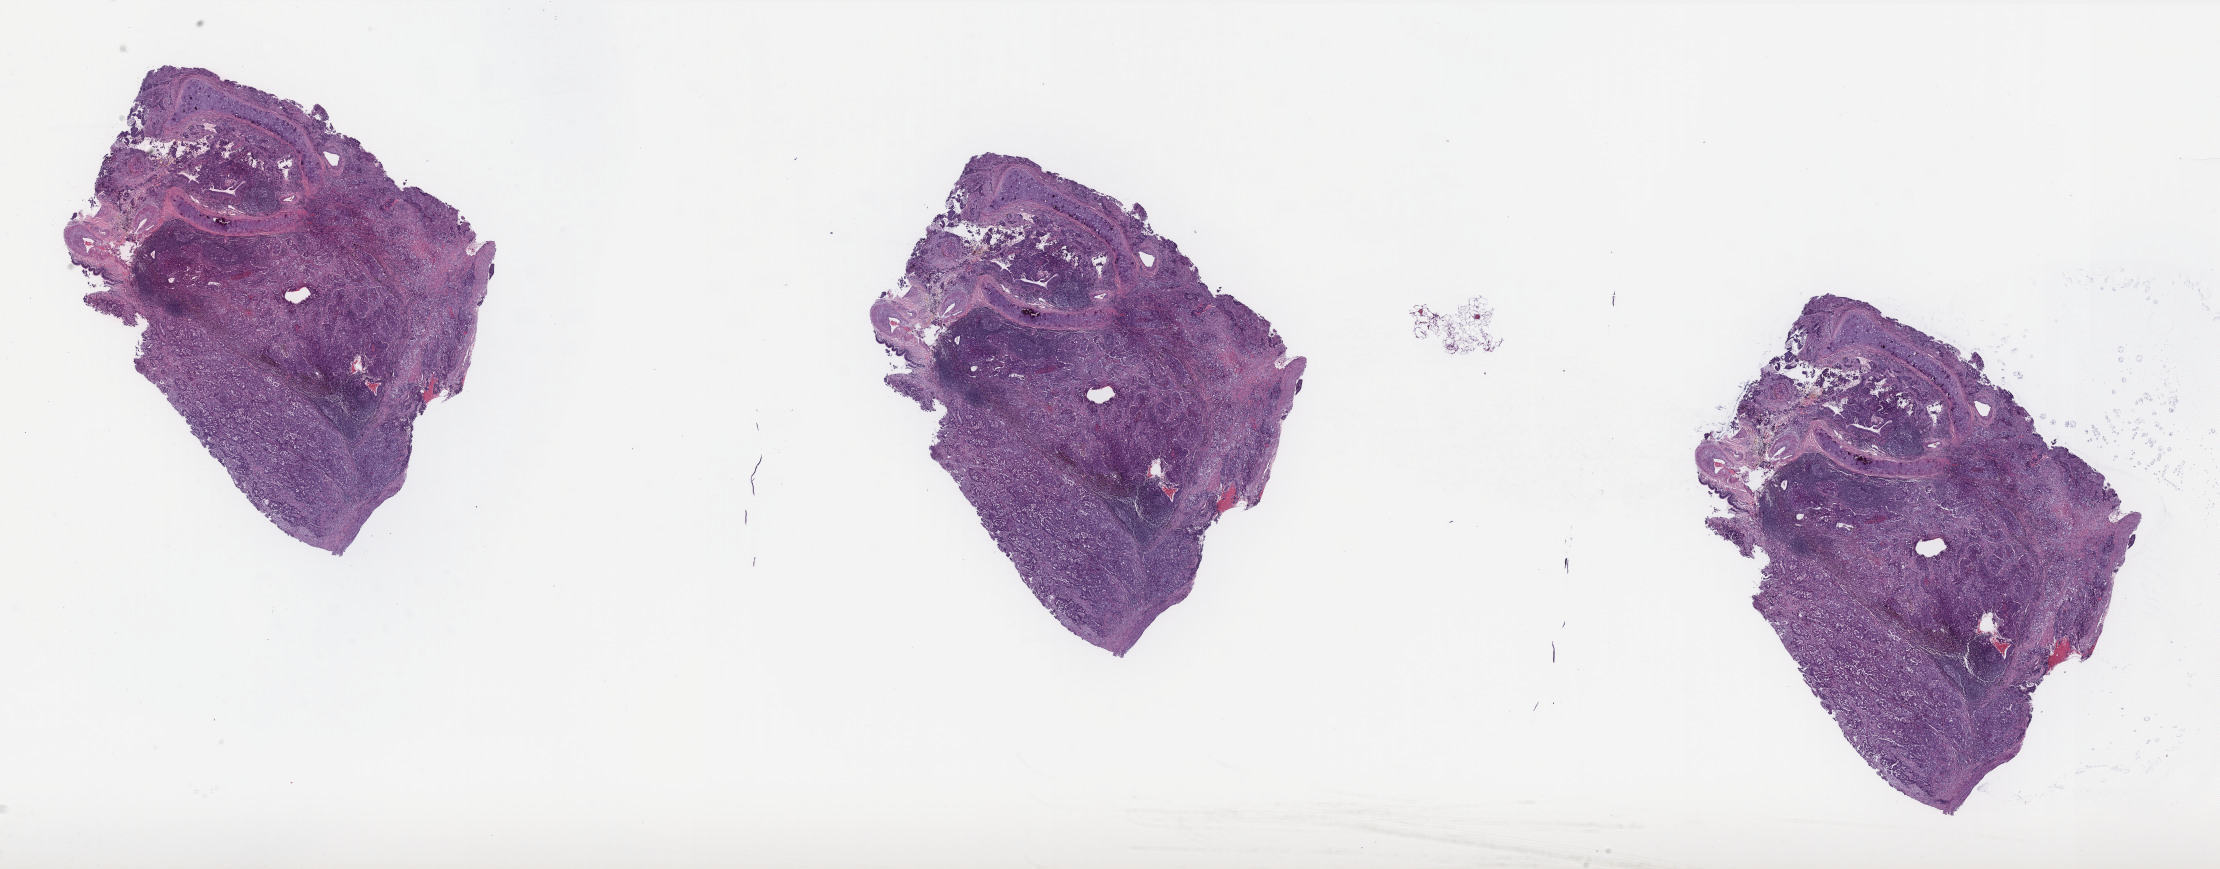
Whole-slide histology image, H&E — whole scanned area (about 35.6 x 13.9 mm) shown as a low-resolution overview, formalin-fixed paraffin-embedded (FFPE) diagnostic section, primary tumour sample from the lung. Patient: female, age at initial diagnosis 78 years.
Diagnosis: Adenocarcinoma, NOS (upper lobe, lung). AJCC pathologic stage: IB (7th edition). Laterality: right.